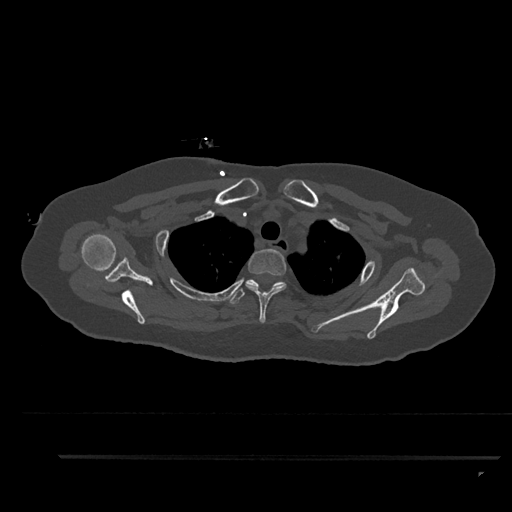
CT including the spine, one axial slice. Position 708 of 797 along the scan axis. Reconstruction kernel Br40s/3. Bone window (W 1800 / L 400 HU). 0.5 mm slice thickness. 512 × 512 image matrix. Patient: female, 44 years. From the clinical record (not read from this slice): primary cancer: renal.
Annotated regions visible in this slice (semi-automatic segmentation, software-assisted and operator-edited):
- T1 vertebra: box from (x=279, y=284) to (x=286, y=287) px
- T2 vertebra: (x=246, y=249)–(x=287, y=323)
- T3 vertebra: (x=229, y=279)–(x=286, y=304)